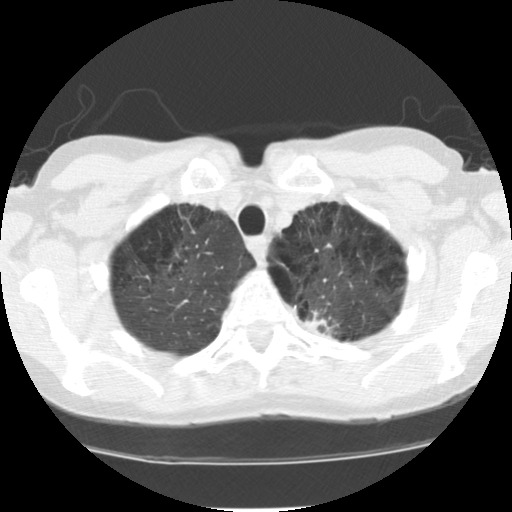
Low-dose screening chest CT, one axial slice. Slice 100 of 116 in the series (ordered by position). Reconstruction kernel STANDARD. 120 kVp. Lung window (W 1500 / L -600 HU). 2.5 mm slice thickness. 512 × 512 image matrix.
Annotated regions visible in this slice (expert manual segmentation):
- lesion 1 (tumor, upper lobe of left lung): bounding box (x1, y1, x2, y2) in pixels: (304, 310, 337, 335)